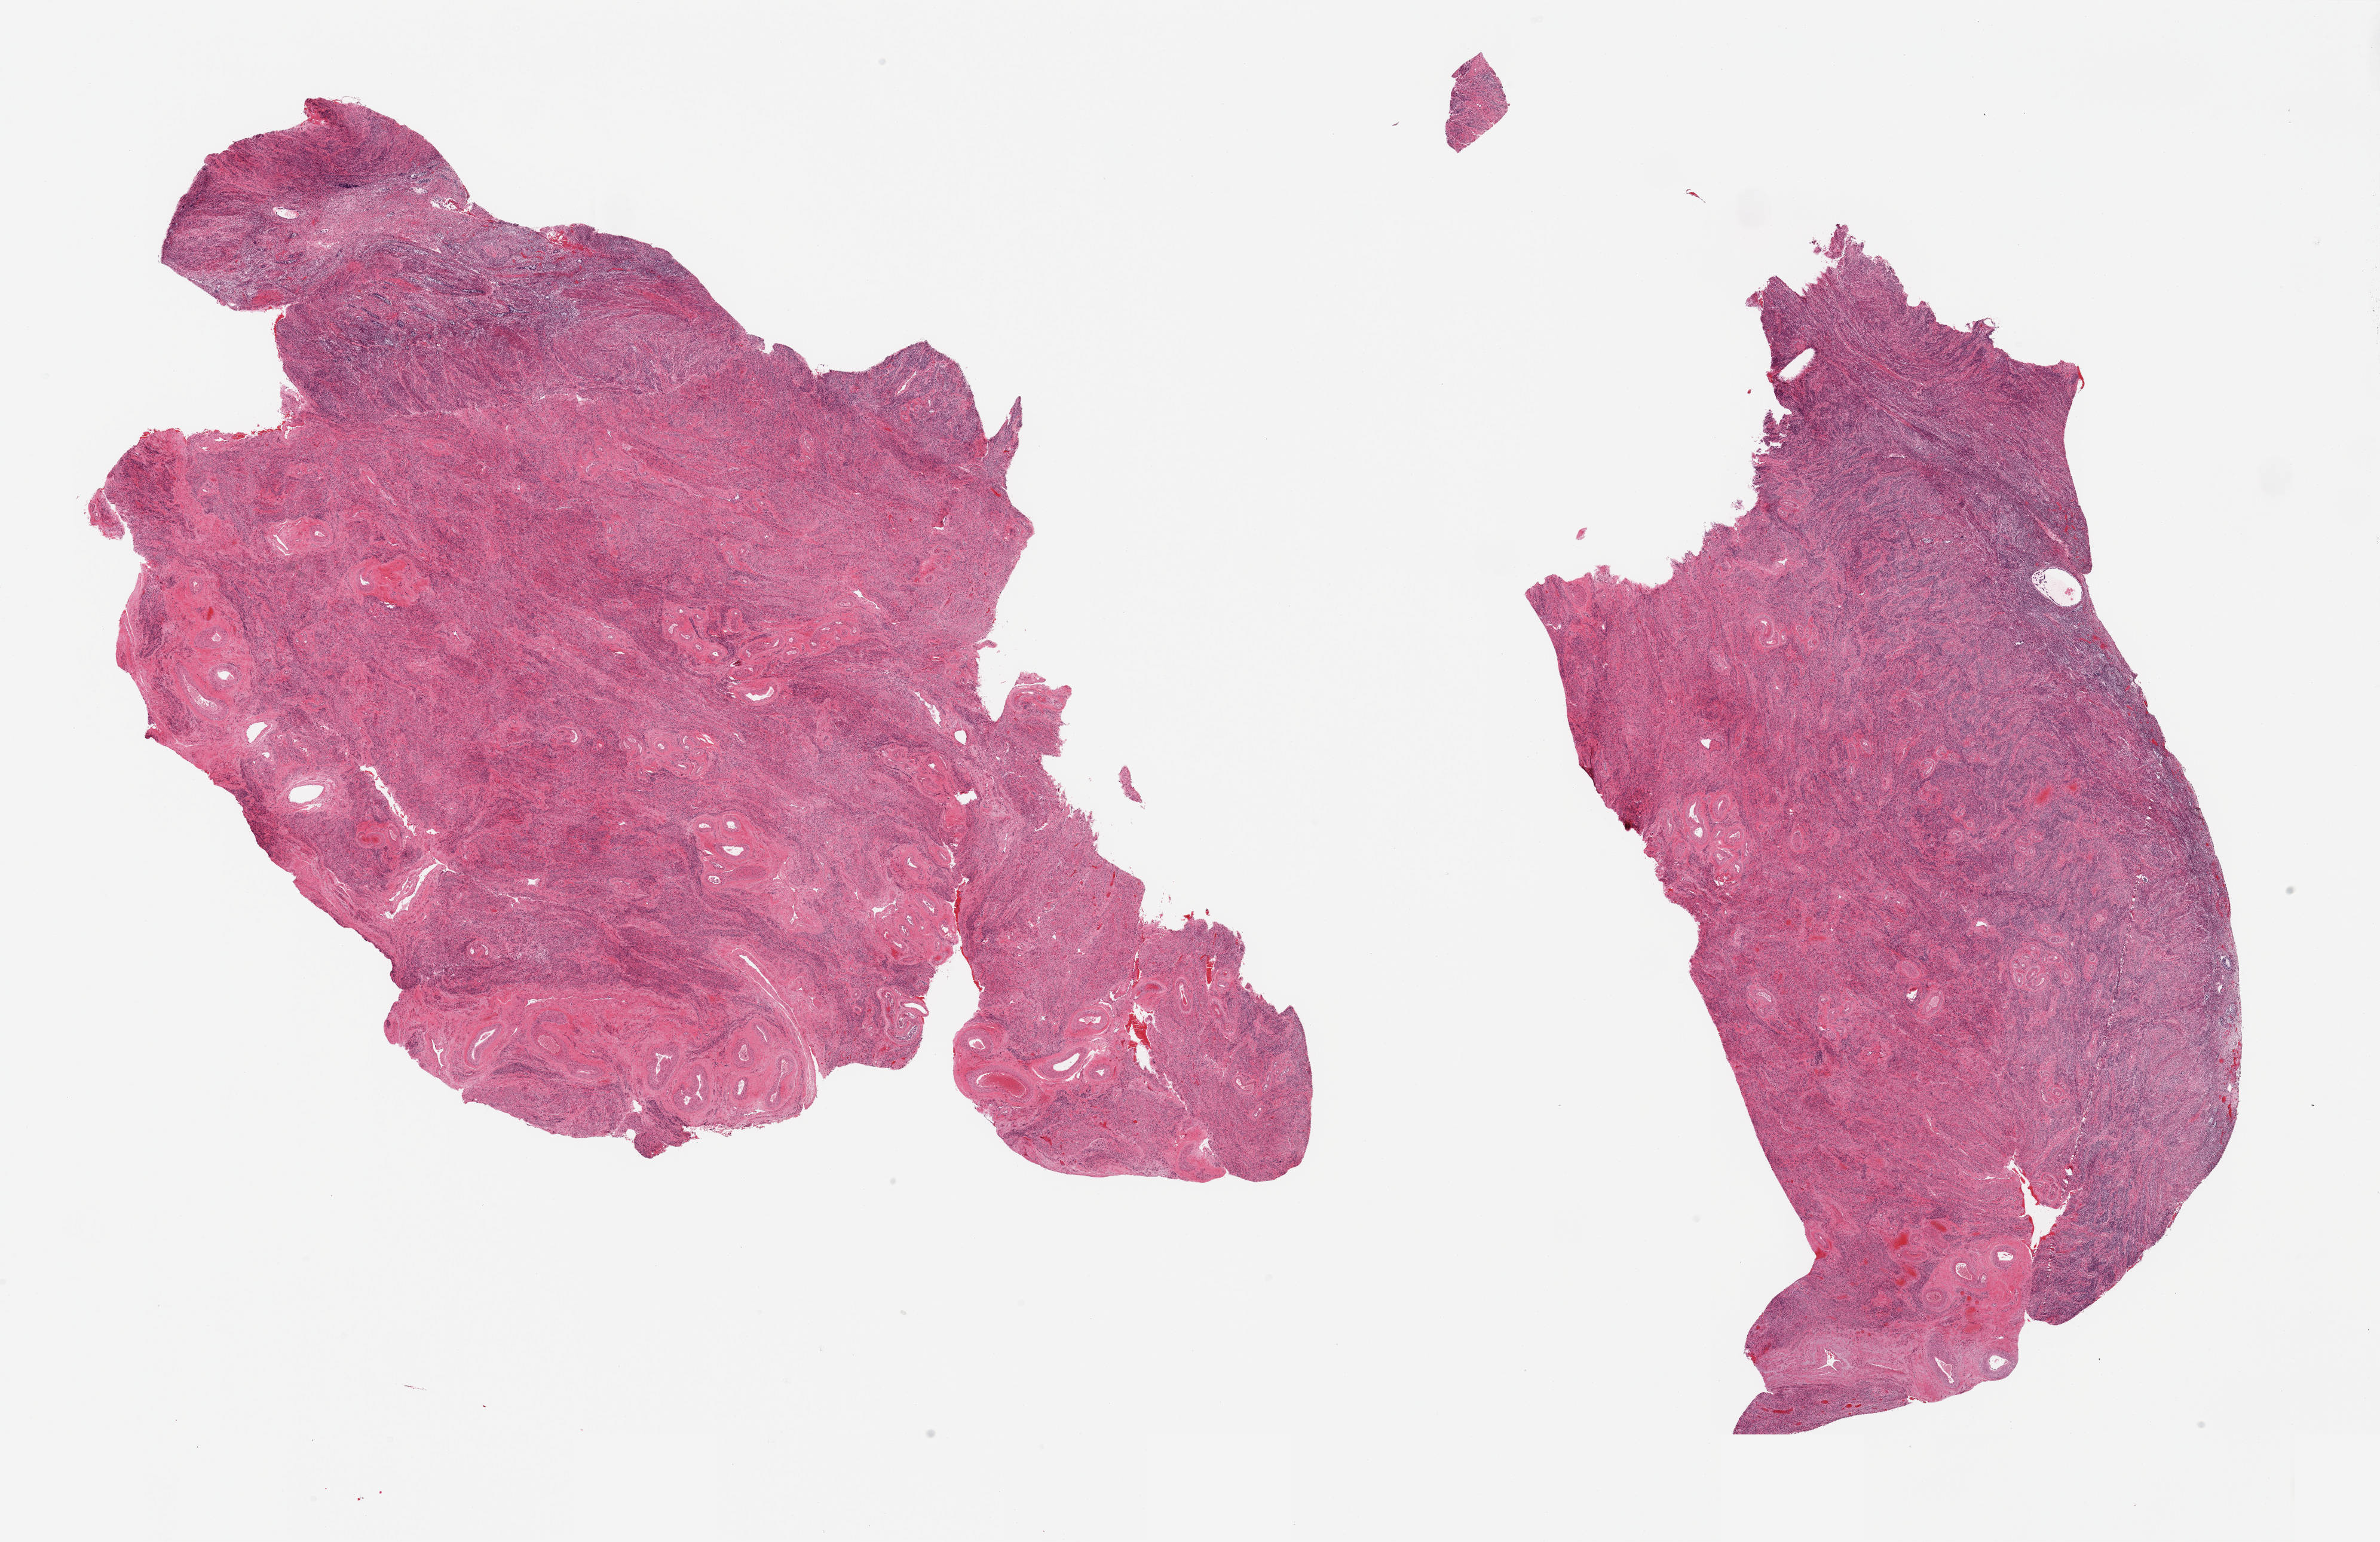
Hematoxylin and eosin (H&E) whole-slide image — a low-resolution overview of the entire scanned area, about 31.5 x 20.4 mm. PAXgene-fixed, paraffin-embedded tissue. Section of uterus (target tissue). Donor tissue sample. Donor: female.
Pathologist's review note for this sample: 2 pieces, myometrium.